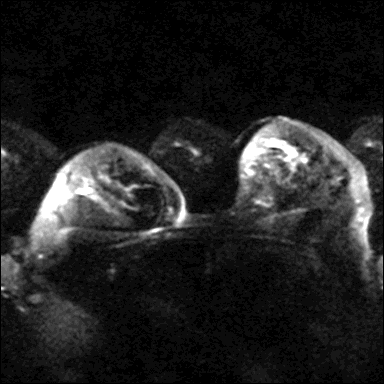
Breast MRI, one axial slice; slice 25 of 40 in the series (ordered by position); diffusion-weighted series; image 2 of 4 stored at this slice position (different b-values; order by instance number); 3 T; 4 mm slice thickness; 384 × 384 image matrix, field of view 320 × 320 mm. Female patient.
Outlined on this slice (outlined manually by an expert reader):
- tumour on diffusion-weighted imaging: bounding box <288,150,294,154> (left, top, right, bottom; pixels)